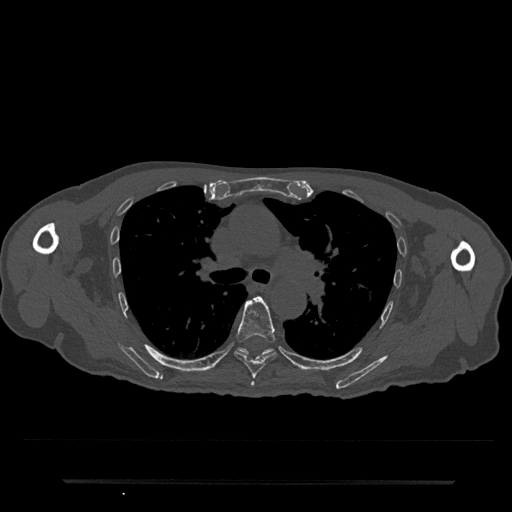
CT including the spine, one axial slice; slice 521 of 797 in the series (ordered by position); bone window (W 1800 / L 400 HU); 0.5 mm slice thickness; 512 × 512 image matrix. Male patient, age 74 years. From the clinical record (not read from this slice): primary cancer: prostate.
Annotated regions visible in this slice (semi-automatic segmentation, software-assisted and operator-edited):
- T5 vertebra: box from (x=251, y=382) to (x=255, y=386) px
- T6 vertebra: (x=234, y=296)–(x=277, y=379)
- T7 vertebra: (x=238, y=348)–(x=274, y=360)